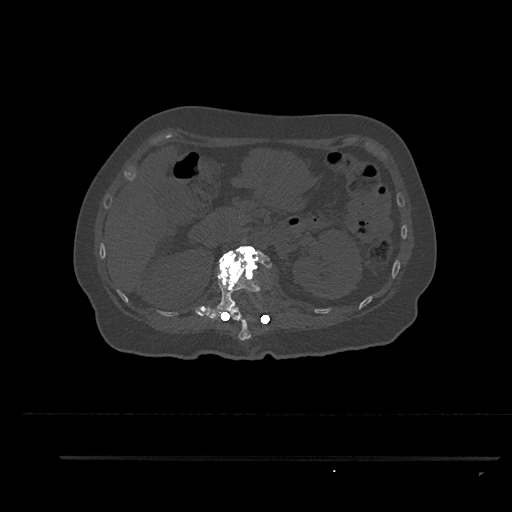
CT including the spine, one axial slice; slice 229 of 797 in the series (ordered by position); bone window (W 1800 / L 400 HU); 0.5 mm slice thickness; 512 × 512 image matrix. Female patient, age 44 years. Case-level facts recorded for this patient, not image findings: primary cancer: renal; vertebrae with lytic lesions (as recorded): L1.
Outlined on this slice (semi-automatically segmented with operator editing):
- L1 vertebra: bounding box (x1, y1, x2, y2) in pixels: (207, 246, 273, 322)
- T12 vertebra: (221, 308, 253, 340)